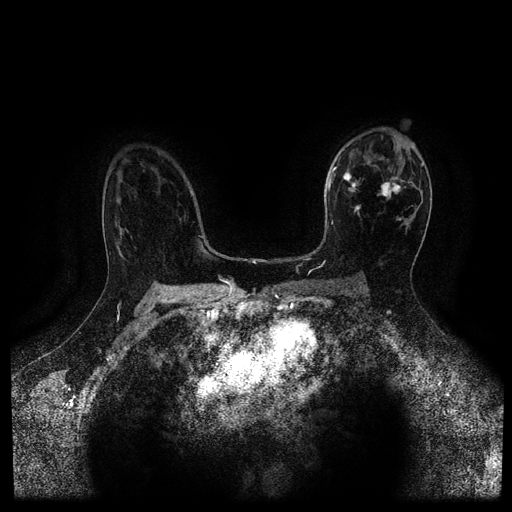
Breast MRI (dynamic contrast-enhanced, multi-phase), one axial slice. Slice 67 of 116 in the series (ordered by position). Dynamic contrast-enhanced series, time point 2 of 5 at this slice position (early post-contrast). 1.5 T. TE 2.7 ms, TR 5.4 ms. 2 mm slice thickness. 512 × 512 image matrix, field of view 340 × 340 mm. Patient: female, 50 years.
Structures marked on this image (semi-automatic segmentation, software-assisted and operator-edited):
- breast lesion (labelled 'tumour' in the annotation; benign lesions carry a separate 'benign' label): bounding box (x1, y1, x2, y2) in pixels: (342, 172, 404, 220)